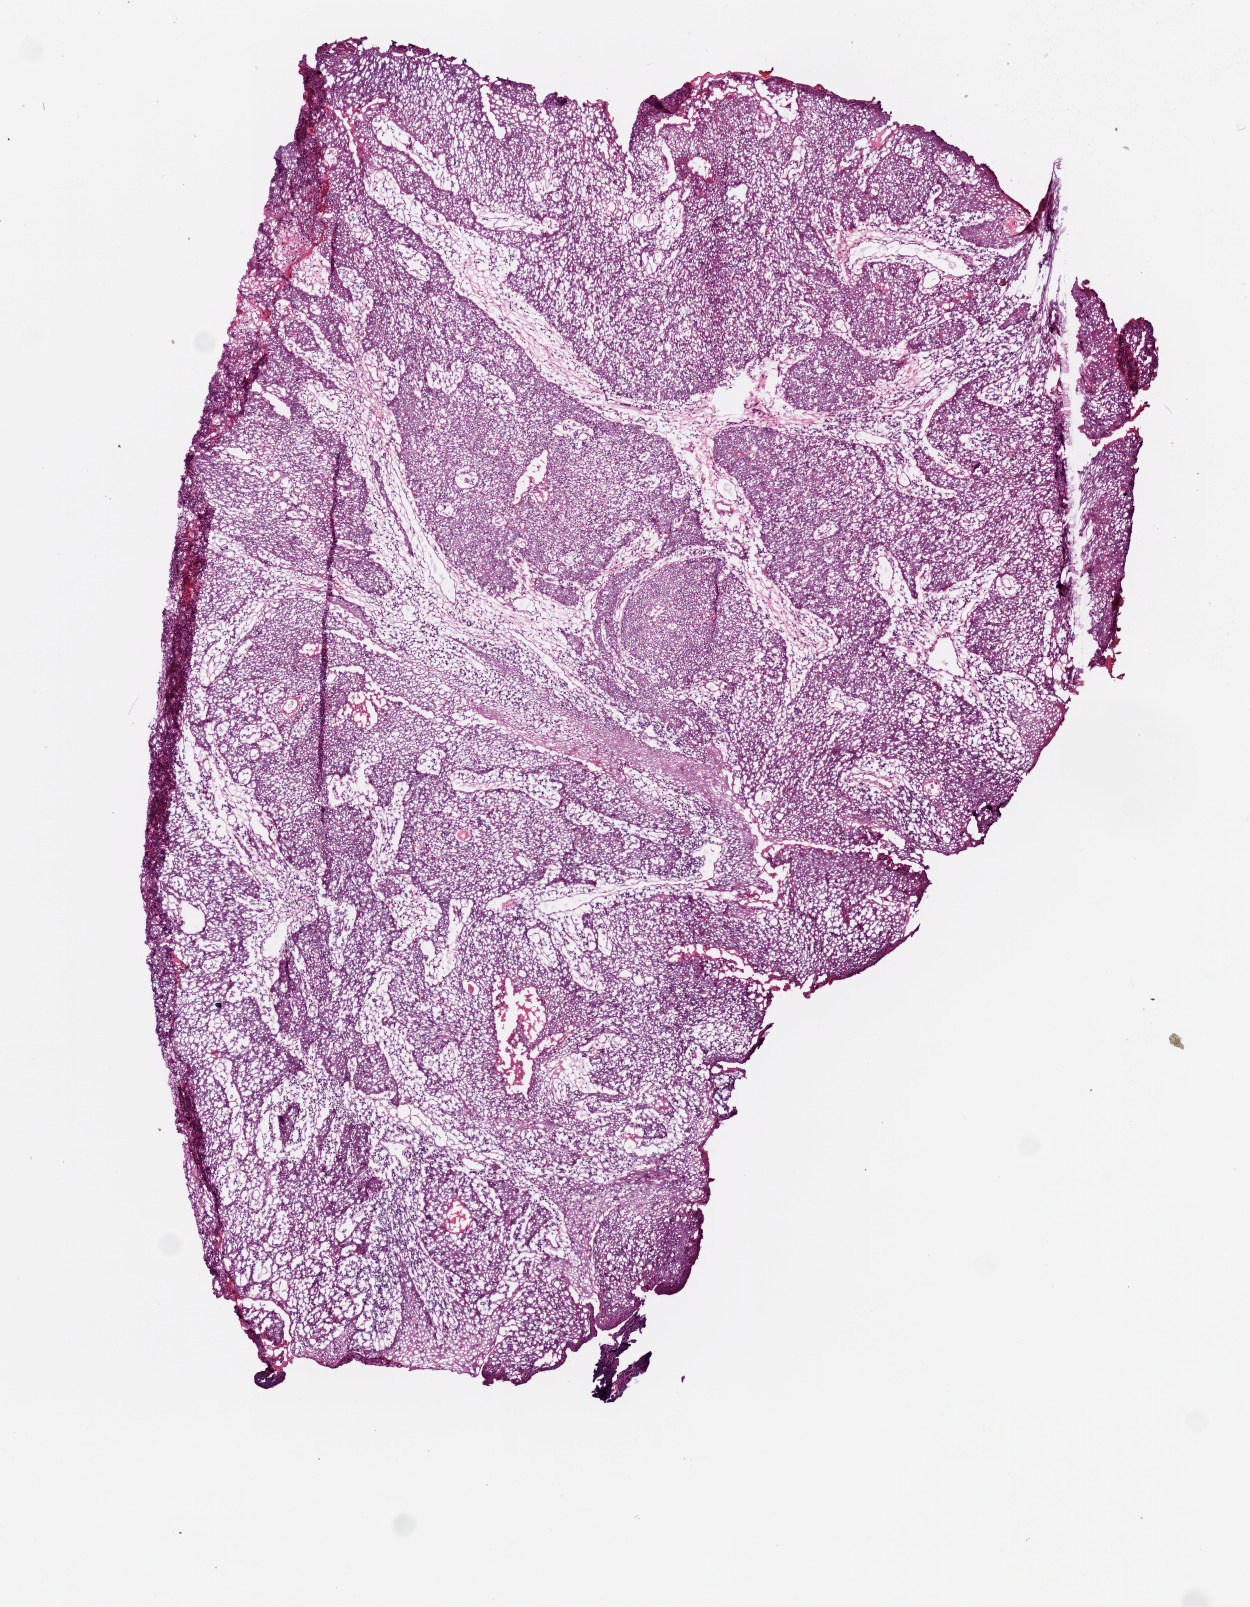
Whole-slide histology image, H&E, a low-resolution overview of the entire scanned area, about 5.0 x 6.4 mm (from a 20x scan). Frozen section from the top of the tissue portion. Sample: primary tumour, head and neck. Male patient; age at initial diagnosis 51 years. Histologic grade: G2 (moderately differentiated). Pathologist review of this section (percent, as recorded): tumour cells 85%, tumour nuclei 80%, normal cells 0%, stromal cells 15%, necrosis 0%.
* diagnosis: Squamous cell carcinoma, NOS (tonsil, NOS)